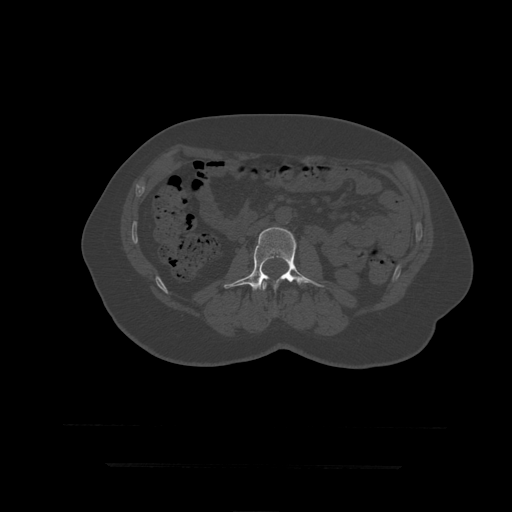
CT including the spine, one axial slice; position 127 of 399 along the scan axis; bone window (W 1800 / L 400 HU); 512 × 512 image matrix, field of view 450 × 450 mm. Patient age 41 years. Case-level facts recorded for this patient, not image findings: primary cancer: breast.
Annotated regions visible in this slice (semi-automatically segmented with operator editing):
- L2 vertebra: bounding box (x1, y1, x2, y2) in pixels: (262, 281, 267, 291)
- L3 vertebra: (224, 228, 324, 292)